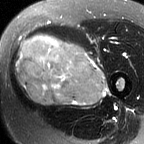
MRI of an extremity soft-tissue mass, one axial slice; slice 29 of 60 in the series (ordered by position); T2-weighted fat-saturated; MR volume resampled by the dataset authors to the PET/CT grid (not the native acquisition matrix); 144 × 144 image matrix, field of view 141 × 141 mm. Female patient. Case-level facts recorded for this patient, not image findings: histological type: pleiomorphic leiomyosarcoma; grade: intermediate; site of the primary tumour: left thigh.
Outlined on this slice (expert contour drawn on MRI and transferred to this co-registered scan by the dataset authors):
- gross tumour volume including surrounding oedema: bounding box (x1, y1, x2, y2) in pixels: (15, 35, 108, 107)
- gross tumour volume (mass): (15, 35, 106, 105)